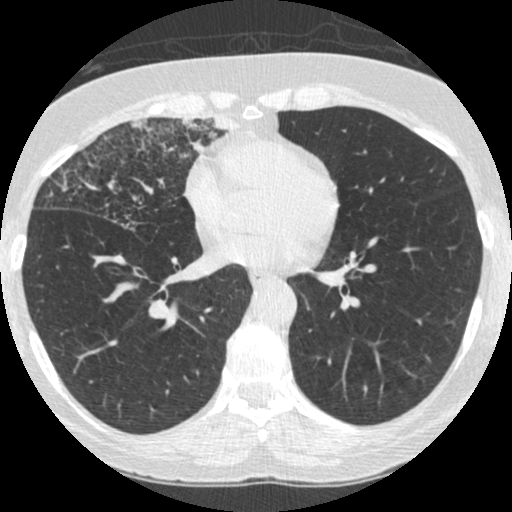
Low-dose screening chest CT, one axial slice; position 118 of 253 along the scan axis; reconstruction kernel STANDARD; 120 kVp; lung window (W 1500 / L -600 HU); 1.25 mm slice thickness; 512 × 512 image matrix, field of view 294 × 294 mm.
Structures marked on this image (manually delineated by an expert):
- lesion 4 (tumor, upper lobe of right lung): bounding box (x1, y1, x2, y2) in pixels: (181, 115, 236, 153)